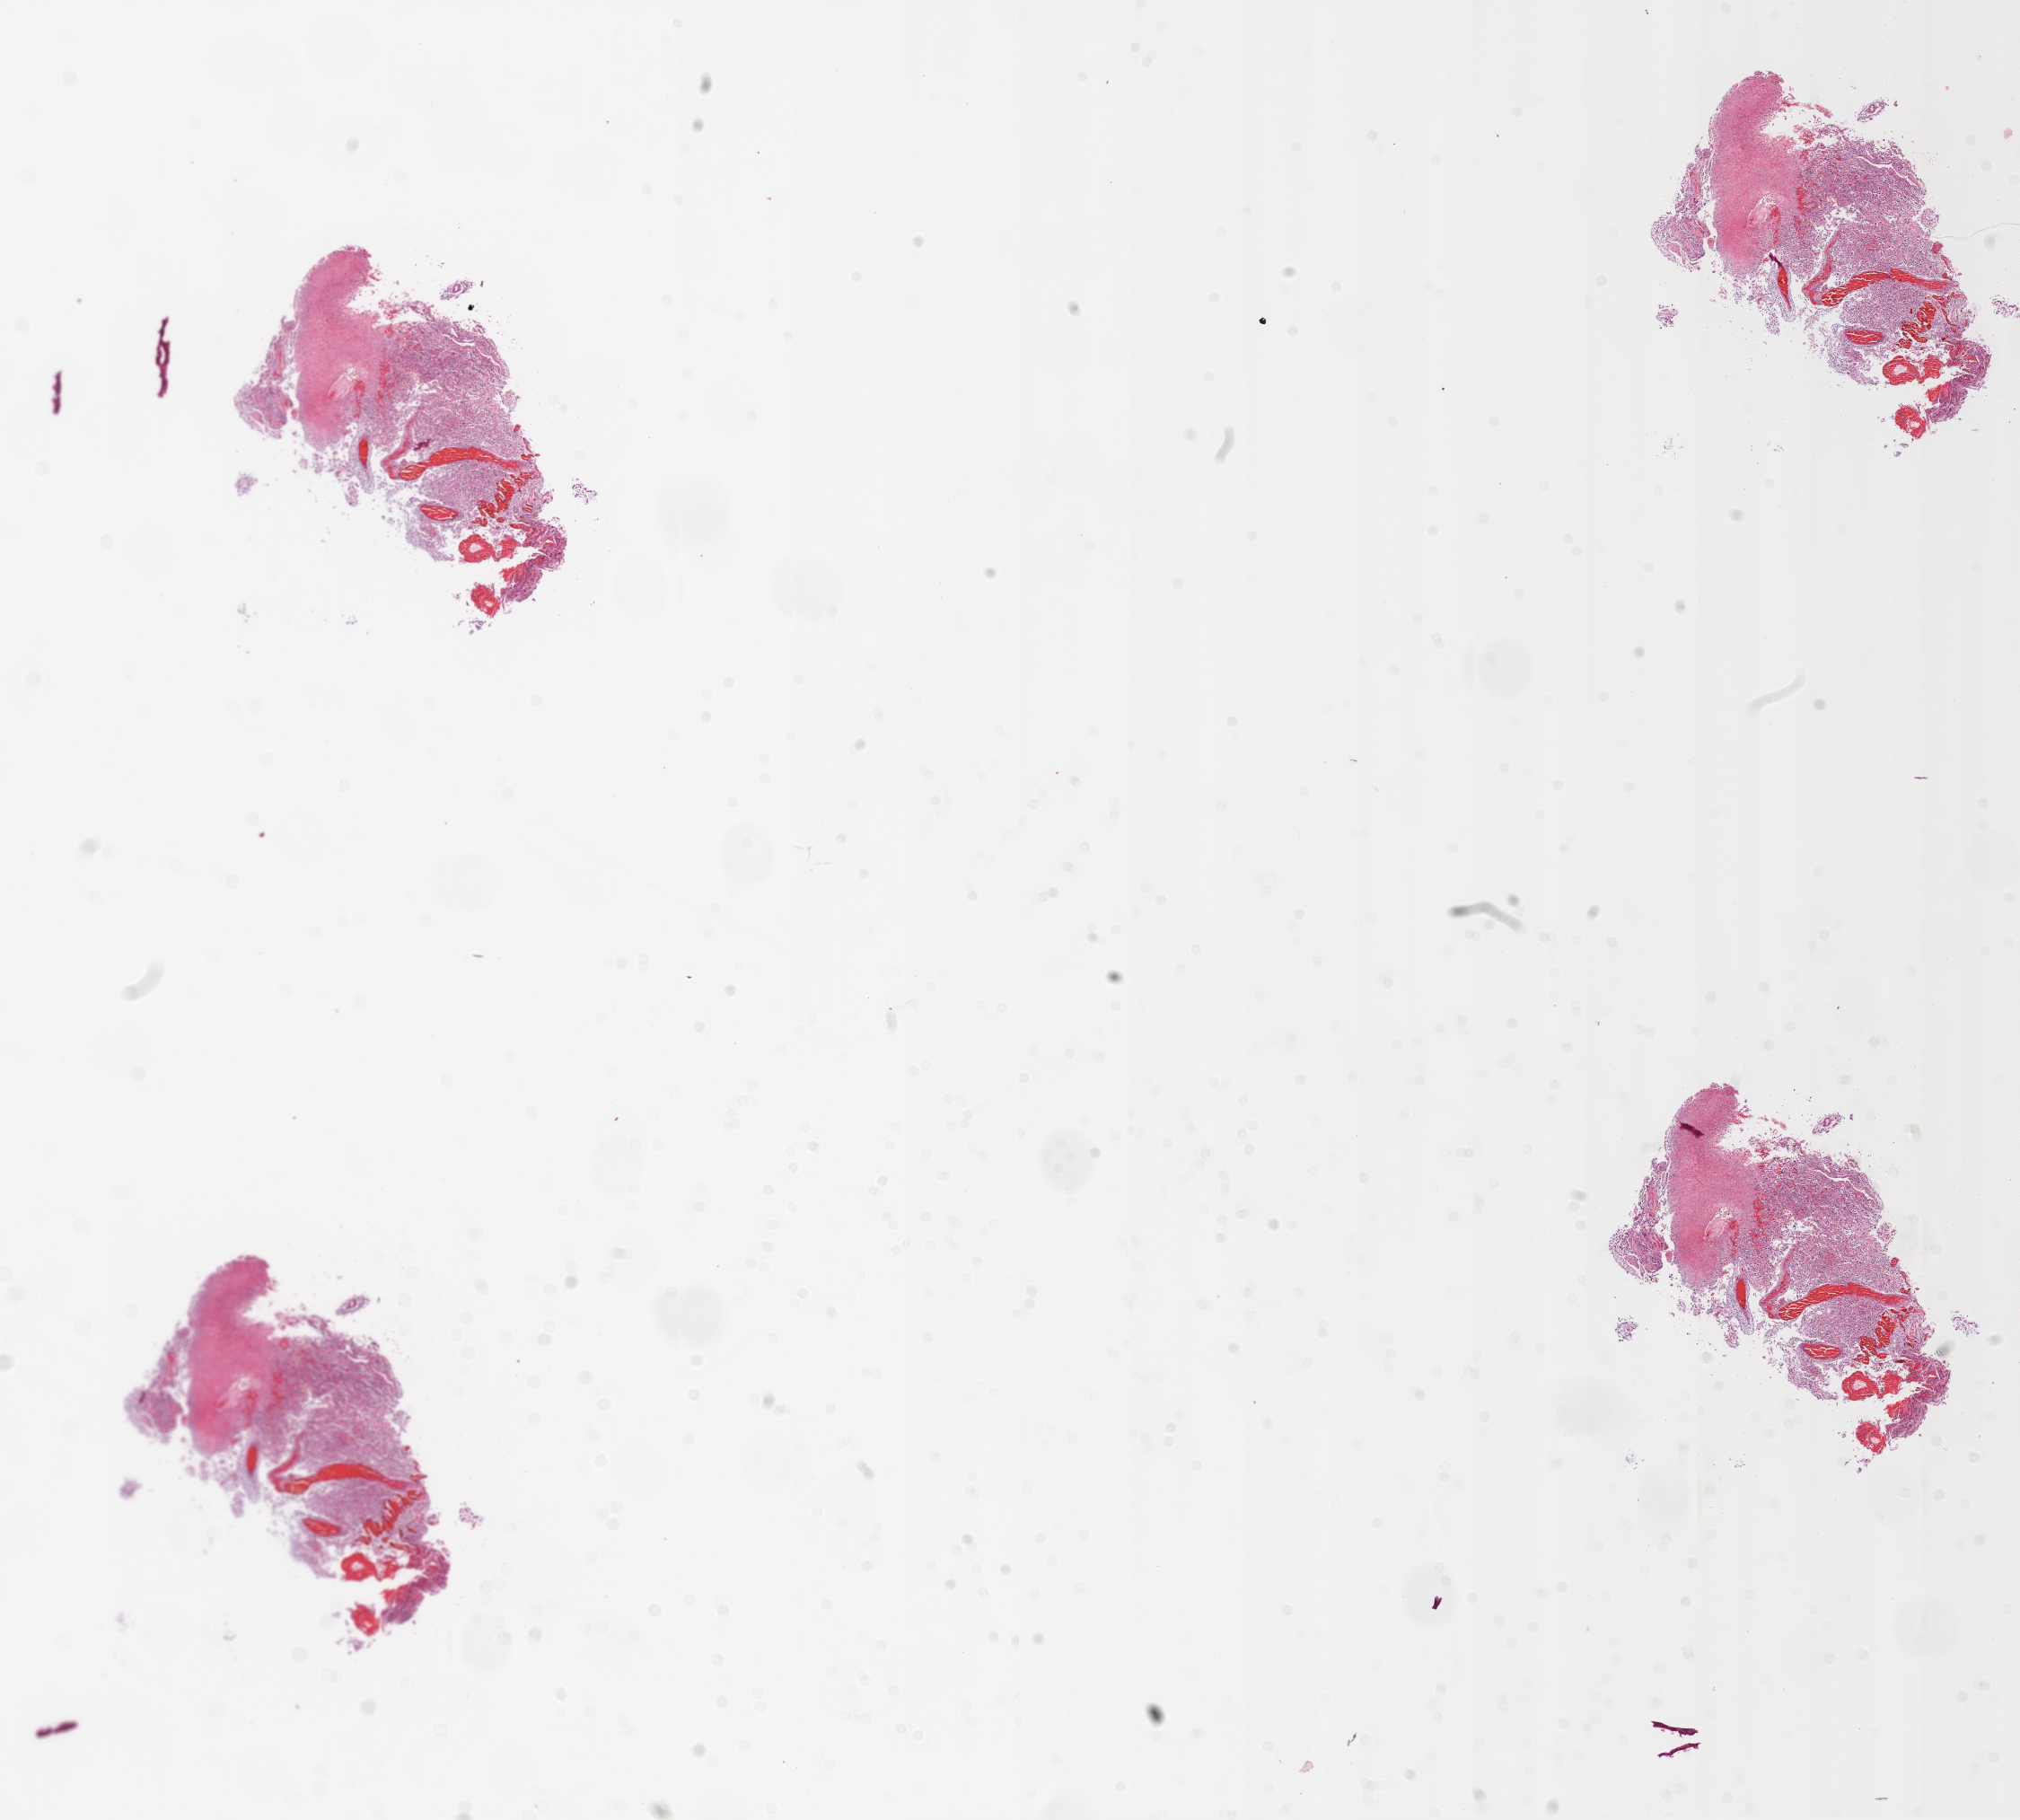
Digitized H&E tissue section (whole slide), low-resolution overview of the scanned area, about 18.1 x 16.3 mm (acquisition: 20x scan), formalin-fixed paraffin-embedded (FFPE) diagnostic section, sample: primary tumour, brain. Male patient; age at initial diagnosis 54 years.
* pathologic diagnosis: Glioblastoma